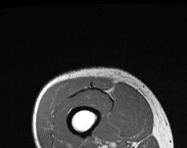
MRI of an extremity soft-tissue mass, one axial slice. Slice 28 of 114 in the series (ordered by position). MR volume resampled by the dataset authors to the PET/CT grid (not the native acquisition matrix). 187 × 148 image matrix. Male patient. From the clinical record (not read from this slice): histological type: pleiomorphic leiomyosarcoma; grade: intermediate; site of the primary tumour: right thigh.
Annotated regions visible in this slice (expert contour drawn on MRI and transferred to this co-registered scan by the dataset authors):
- gross tumour volume including surrounding oedema: bounding box [x1, y1, x2, y2] px = [95, 79, 112, 91]